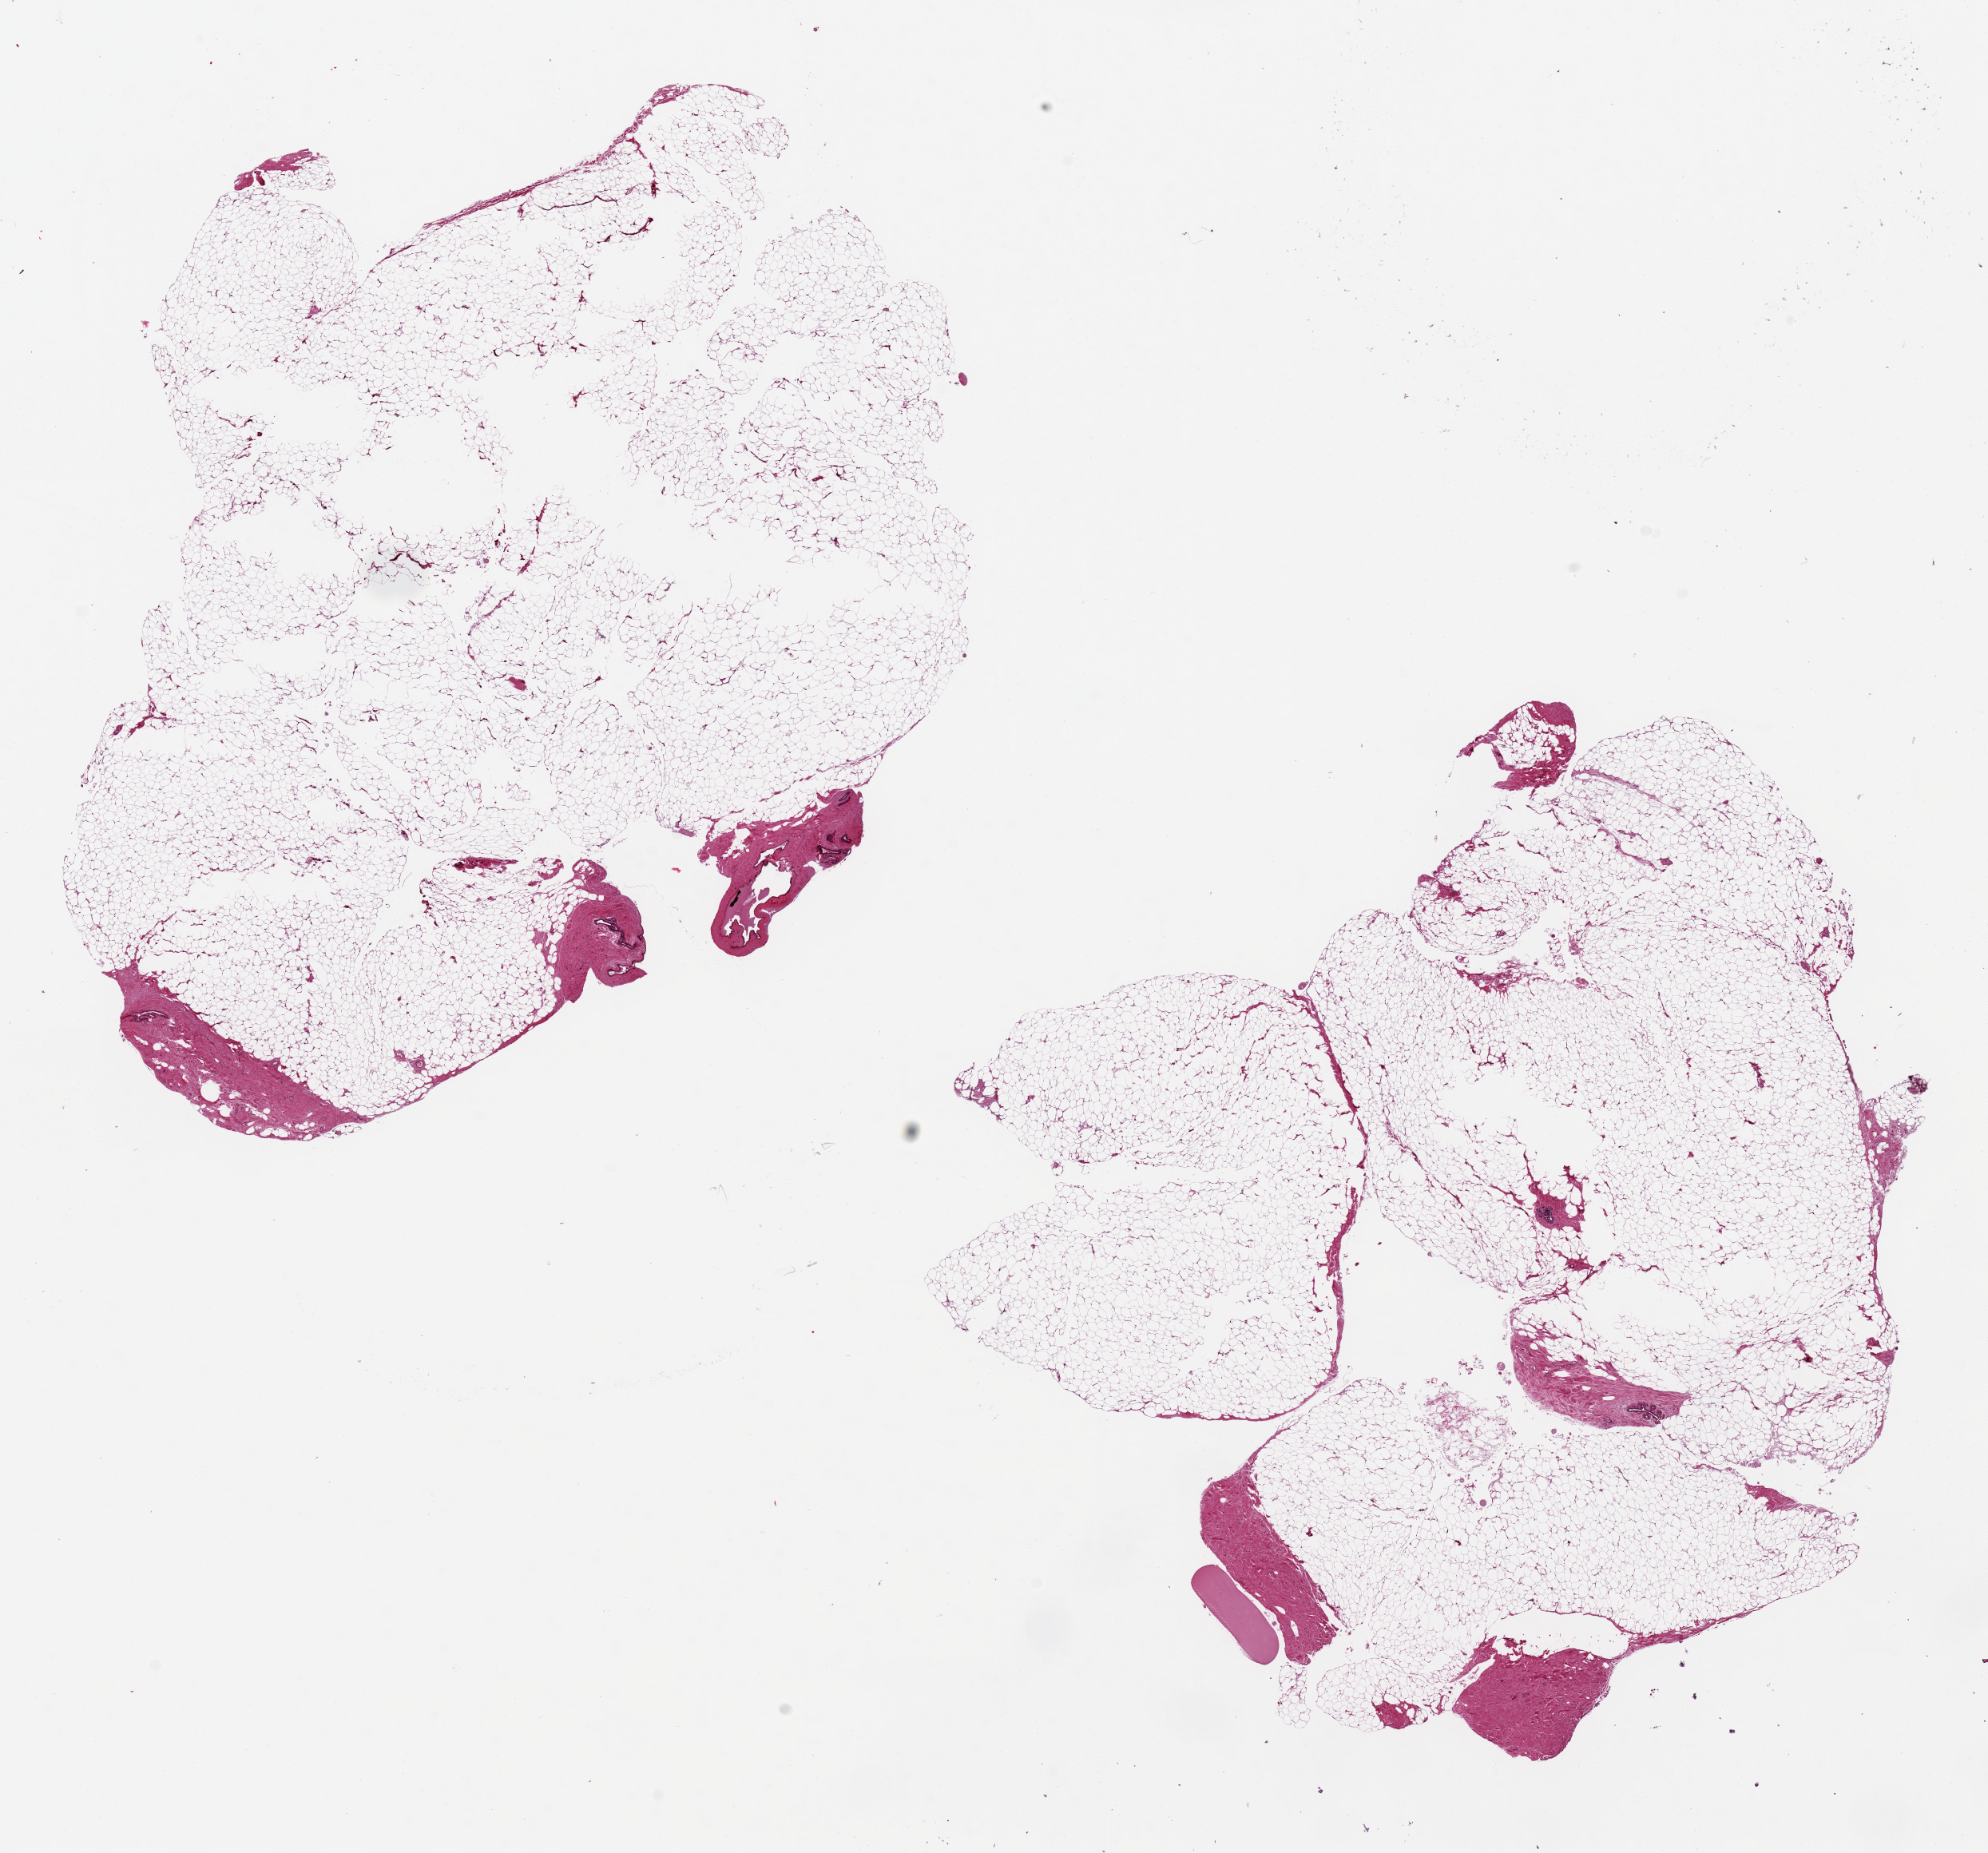
Whole-slide image, H&E stain, whole scanned area (about 19.7 x 18.4 mm, slide scanned at 20x) shown as a low-resolution overview, PAXgene-fixed paraffin-embedded (PFPE) section, sampled site (target tissue): breast, tissue donor sample.
Pathologist's review note for this sample: 2 aliquots, ~10x8mm. Few minute ductal-lobular foci present, >99% adipose tissue.